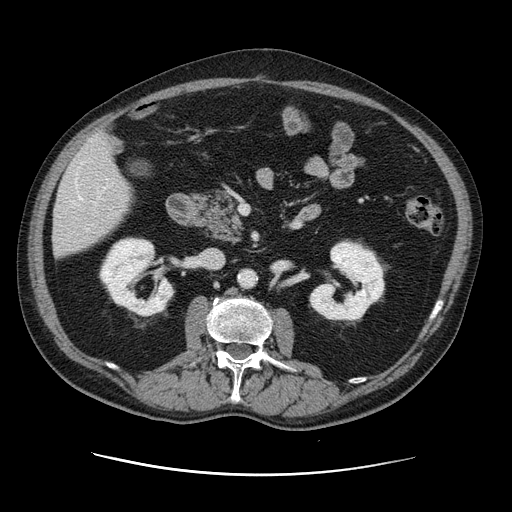
Contrast-enhanced abdominal CT, one axial slice. Intravenous contrast given. Soft-tissue window (W 400 / L 40 HU). 512 × 512 image matrix, field of view 395 × 395 mm. Male patient, age 72 years. From the clinical record (not read from this slice): diagnosis: colorectal cancer liver metastases, imaged before liver resection; multiple liver metastases: yes; largest metastasis: 5.4 cm; disease in both lobes: yes.
Annotated regions visible in this slice (expert manual segmentation):
- hepatic veins: box from (x=72, y=196) to (x=101, y=230) px
- liver: (x=54, y=136)–(x=133, y=257)
- planned liver remnant (the part of the liver to remain after resection): (x=54, y=163)–(x=132, y=257)
- portal vein (with intrahepatic branches): (x=98, y=196)–(x=103, y=200)